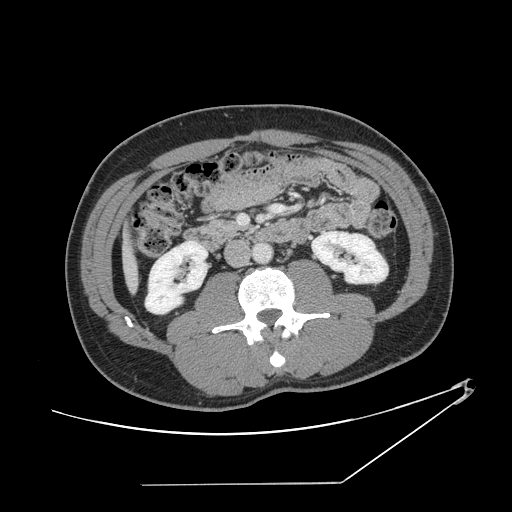
Contrast-enhanced abdominal CT, one axial slice; position 42 of 152 along the scan axis; reconstruction kernel STANDARD; intravenous contrast given; soft-tissue window (W 400 / L 40 HU); 512 × 512 image matrix, field of view 432 × 432 mm. Male patient, age 45 years. Case-level facts recorded for this patient, not image findings: diagnosis: colorectal cancer liver metastases, imaged before liver resection; multiple liver metastases: no; largest metastasis: 1 cm.
Annotated regions visible in this slice (outlined manually by an expert reader):
- liver: bounding box [x1, y1, x2, y2] px = [125, 245, 137, 288]
- planned liver remnant (the part of the liver to remain after resection): [125, 244, 137, 288]